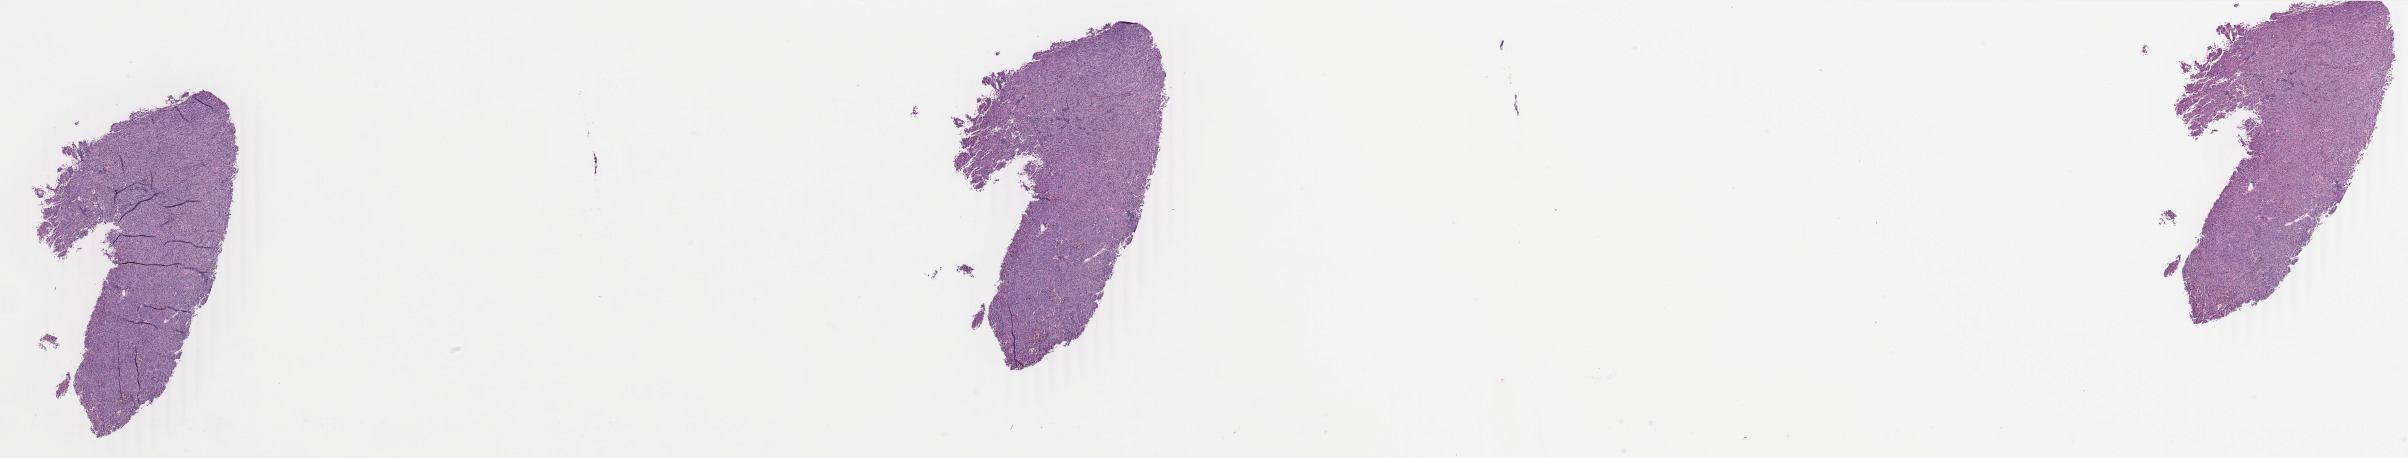
Whole-slide histology image, H&E, a low-resolution overview of the entire scanned area, about 38.3 x 7.3 mm (from a 40x scan); FFPE section; primary tumour sample from the skin. Patient: male, age at initial diagnosis 68 years.
Histologic diagnosis: Malignant melanoma, NOS.